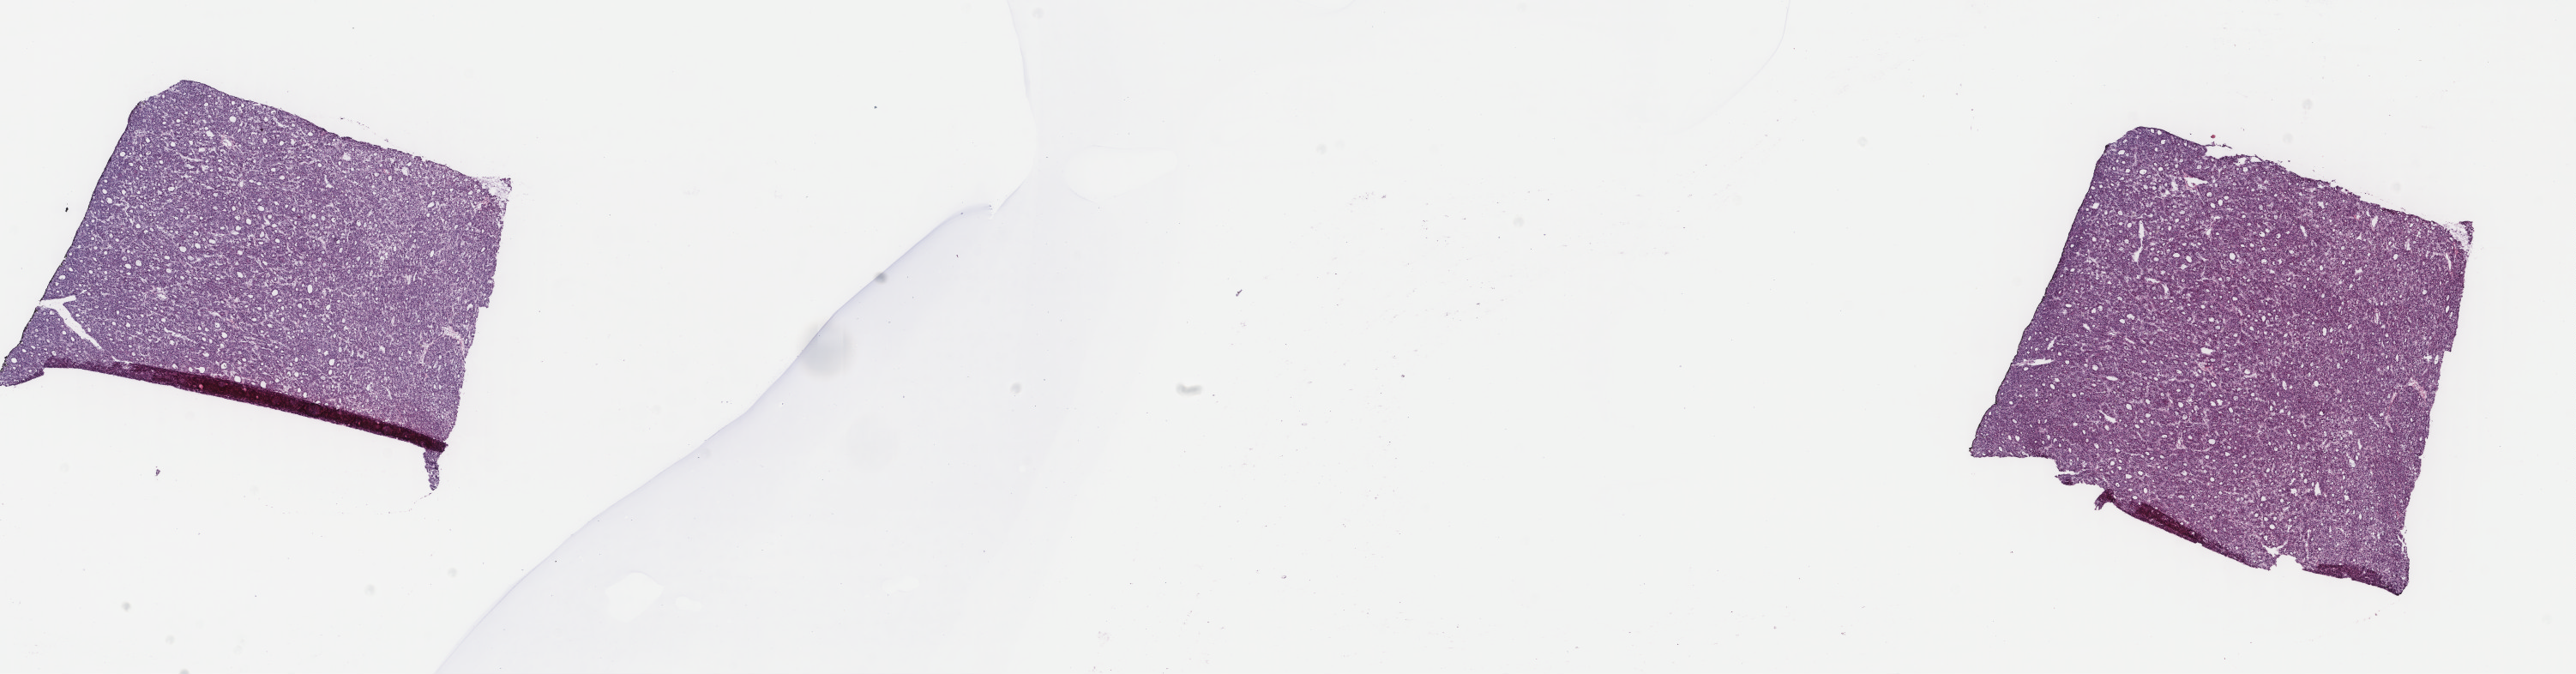
Hematoxylin and eosin (H&E) stained whole-slide image — a low-resolution overview of the entire scanned area, about 23.8 x 6.2 mm (from a 40x scan). Frozen section from the top of the tissue portion. Sample: primary tumour, liver. Male, age 70 years at initial diagnosis. Histologic grade: G2 (moderately differentiated). Composition of this section per pathologist review: tumour cells 95%, tumour nuclei 95%, normal cells 0%, stromal cells 5%, necrosis 0%. Inflammatory infiltration, as recorded: lymphocyte infiltration 0%, monocyte infiltration 1%, neutrophil infiltration 0%.
Histologic diagnosis: Hepatocellular carcinoma, NOS. AJCC pathologic stage: I (7th edition).